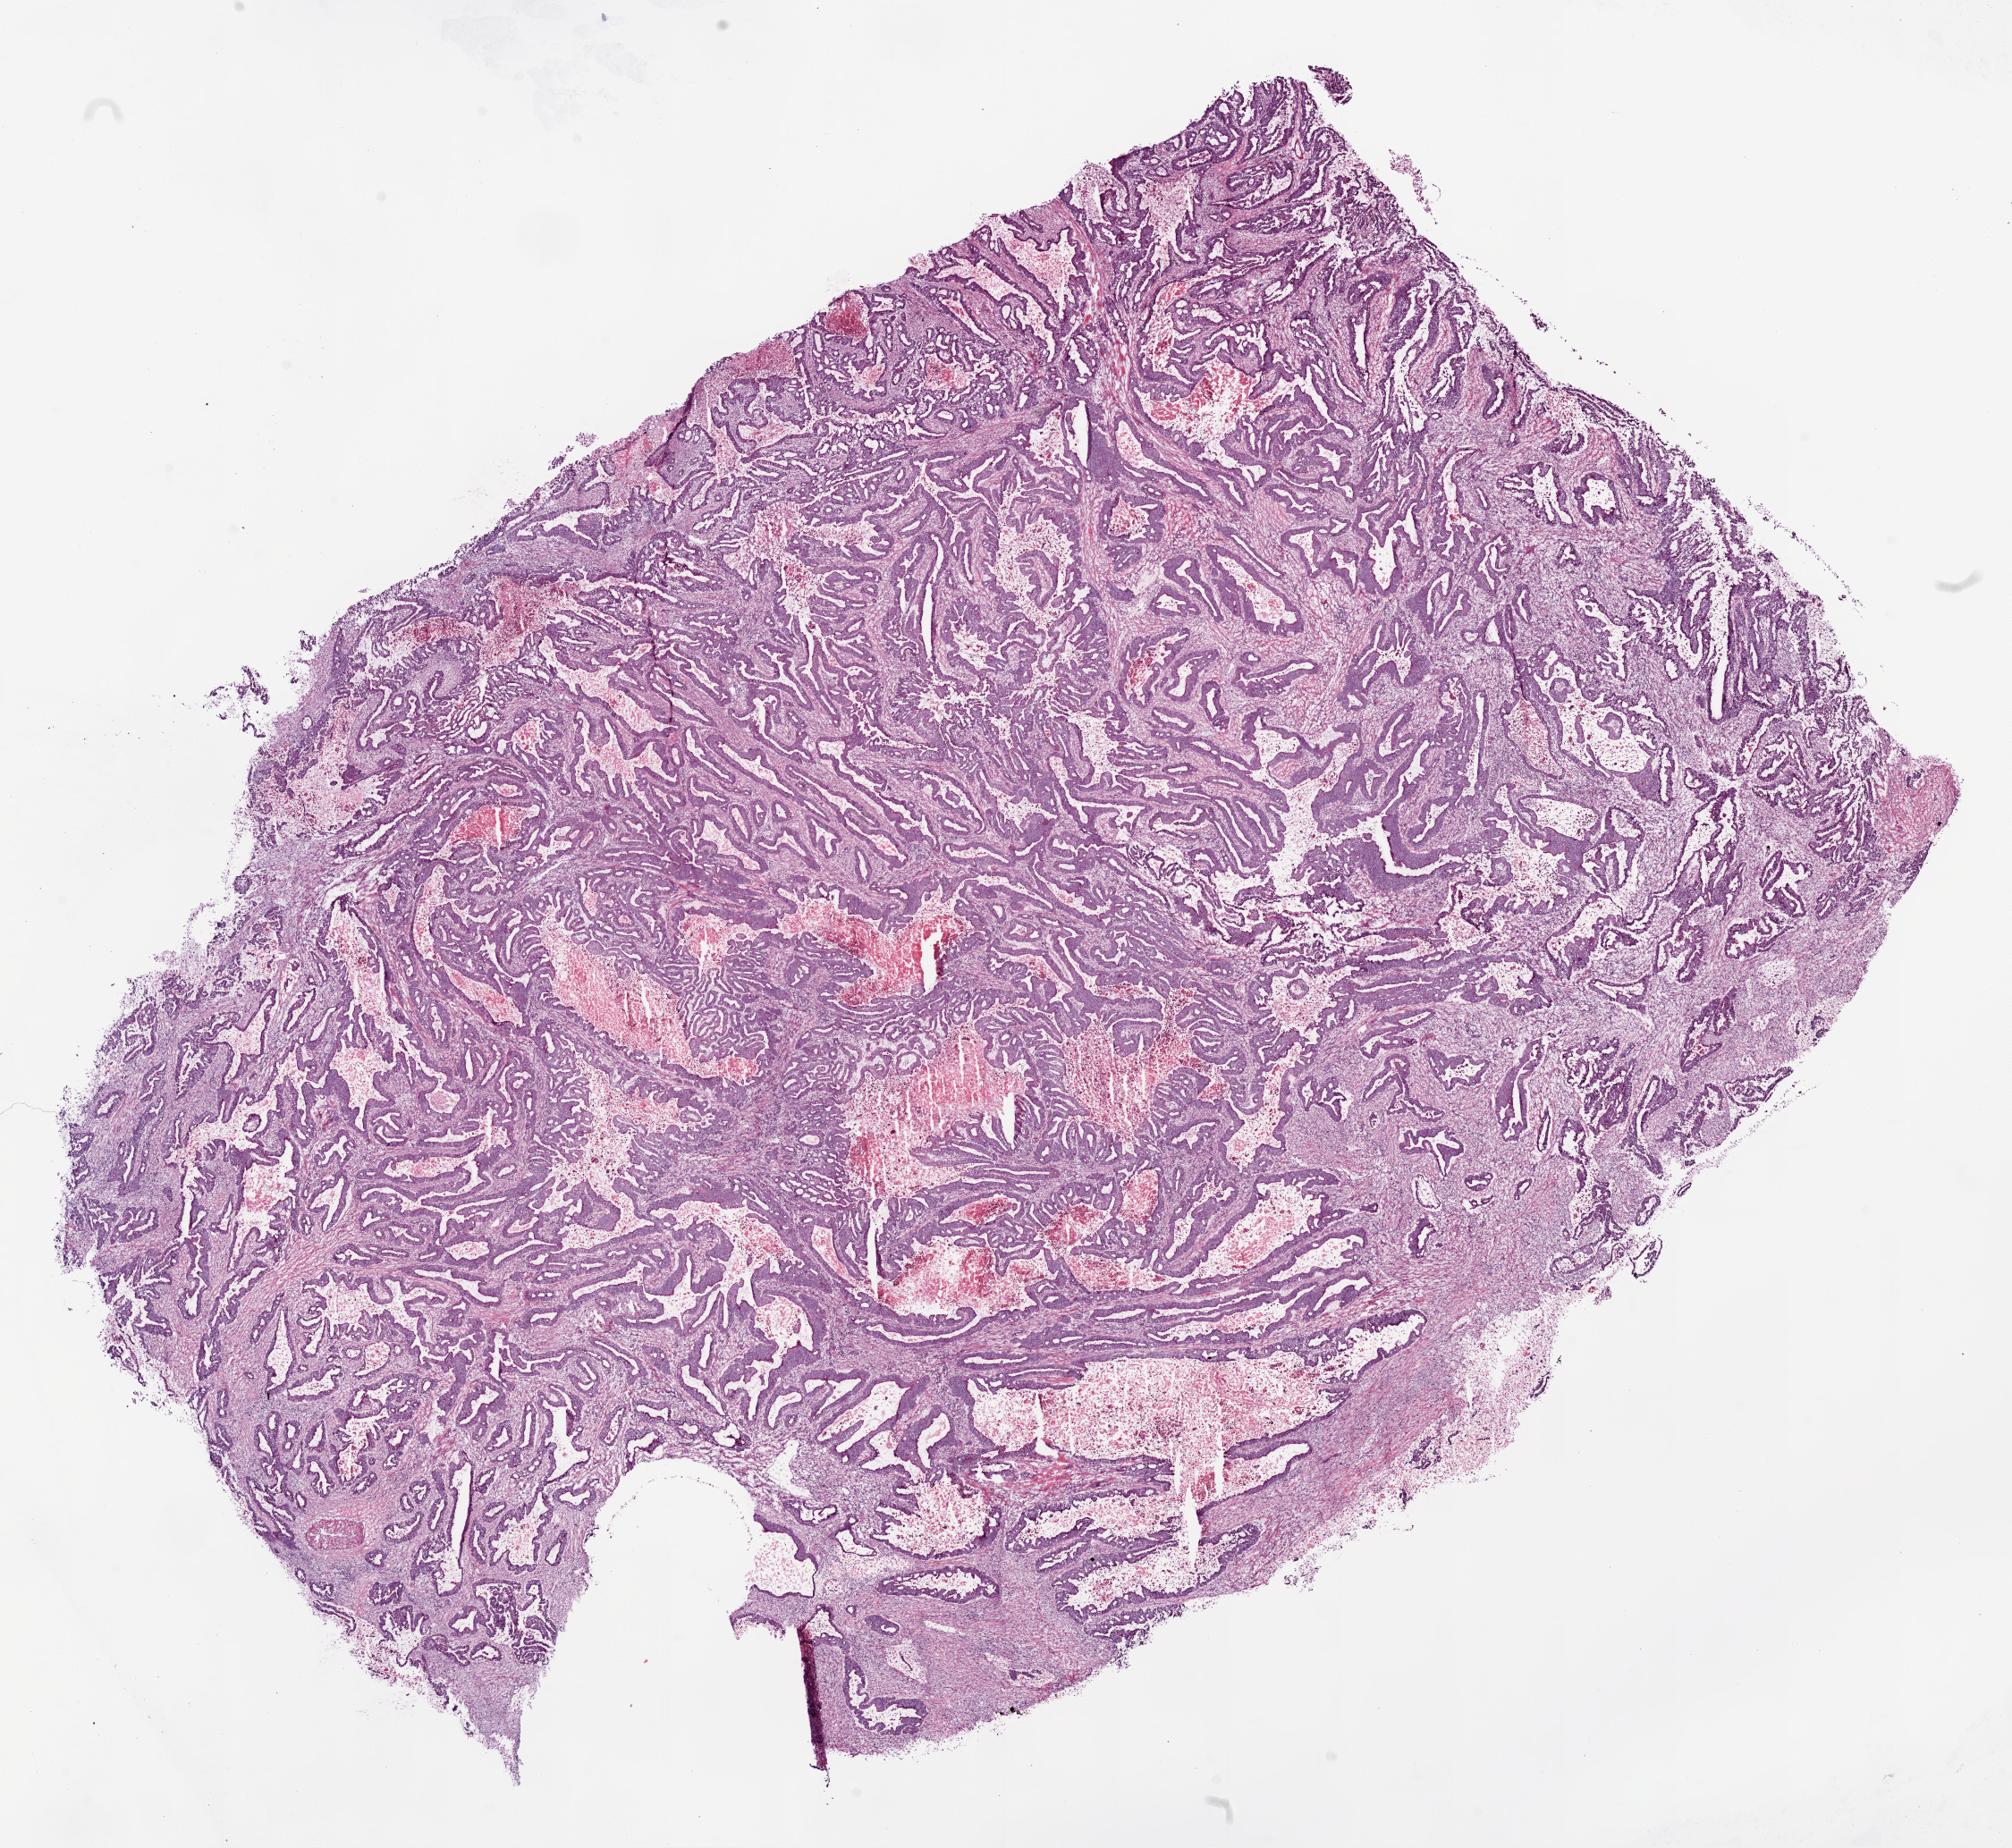
H&E whole-slide image — whole scanned area (about 18.1 x 16.6 mm, from a 20x scan) shown as a low-resolution overview; frozen section; sample: primary tumour, colon. Female patient; age at initial diagnosis 42 years. Composition of this section per pathologist review: tumour cells 65%, tumour nuclei 75%, normal cells 0%, stromal cells 15%, necrosis 20%.
* AJCC pathologic stage: IIA (6th edition)
* pathologic diagnosis: Adenocarcinoma, NOS